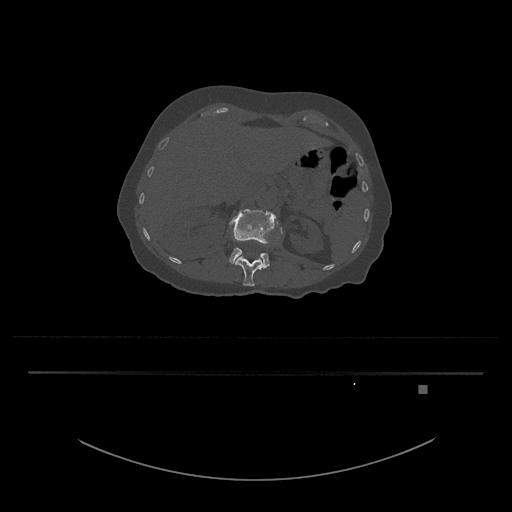
CT including the spine, one axial slice; slice 526 of 797 in the series (ordered by position); reconstruction kernel Br40s/3; 120 kVp; bone window (W 1800 / L 400 HU); 0.5 mm slice thickness; 512 × 512 image matrix, field of view 500 × 500 mm. Female patient, age 57 years. Case-level facts recorded for this patient, not image findings: primary cancer: cervical.
Structures marked on this image (semi-automatically segmented with operator editing):
- L1 vertebra: box from (x=234, y=227) to (x=283, y=286) px